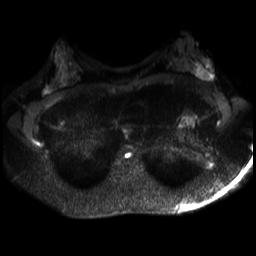
Breast MRI, one axial slice. Slice 17 of 30 in the series (ordered by position). Diffusion-weighted series; image 2 of 4 stored at this slice position (different b-values; order by instance number). 3 T. 256 × 256 image matrix. Female patient.
Annotated regions visible in this slice (manually delineated by an expert):
- tumour on diffusion-weighted imaging: bounding box (x1, y1, x2, y2) in pixels: (199, 62, 210, 78)